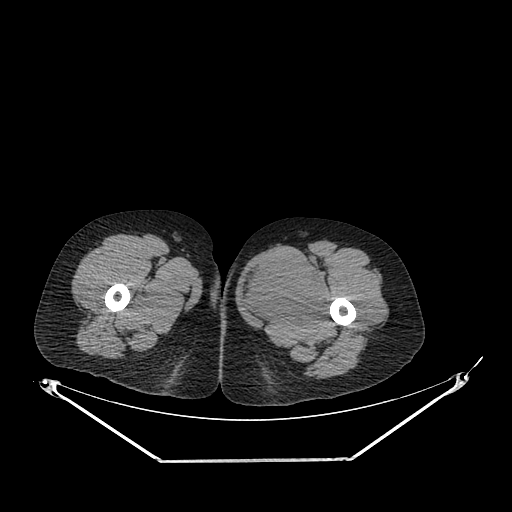
CT of an extremity soft-tissue mass (from a PET/CT study), one axial slice; position 245 of 267 along the scan axis; reconstruction kernel SOFT; soft-tissue window (W 400 / L 40 HU); 3.75 mm slice thickness; 512 × 512 image matrix, field of view 500 × 500 mm. Female patient. Case-level facts recorded for this patient, not image findings: histological type: pleiomorphic leiomyosarcoma; grade: intermediate; site of the primary tumour: left thigh.
Outlined on this slice (expert contour drawn on MRI and transferred to this co-registered scan by the dataset authors):
- gross tumour volume including surrounding oedema: bounding box (x1, y1, x2, y2) in pixels: (240, 258, 328, 327)
- gross tumour volume (mass): (240, 258, 328, 325)